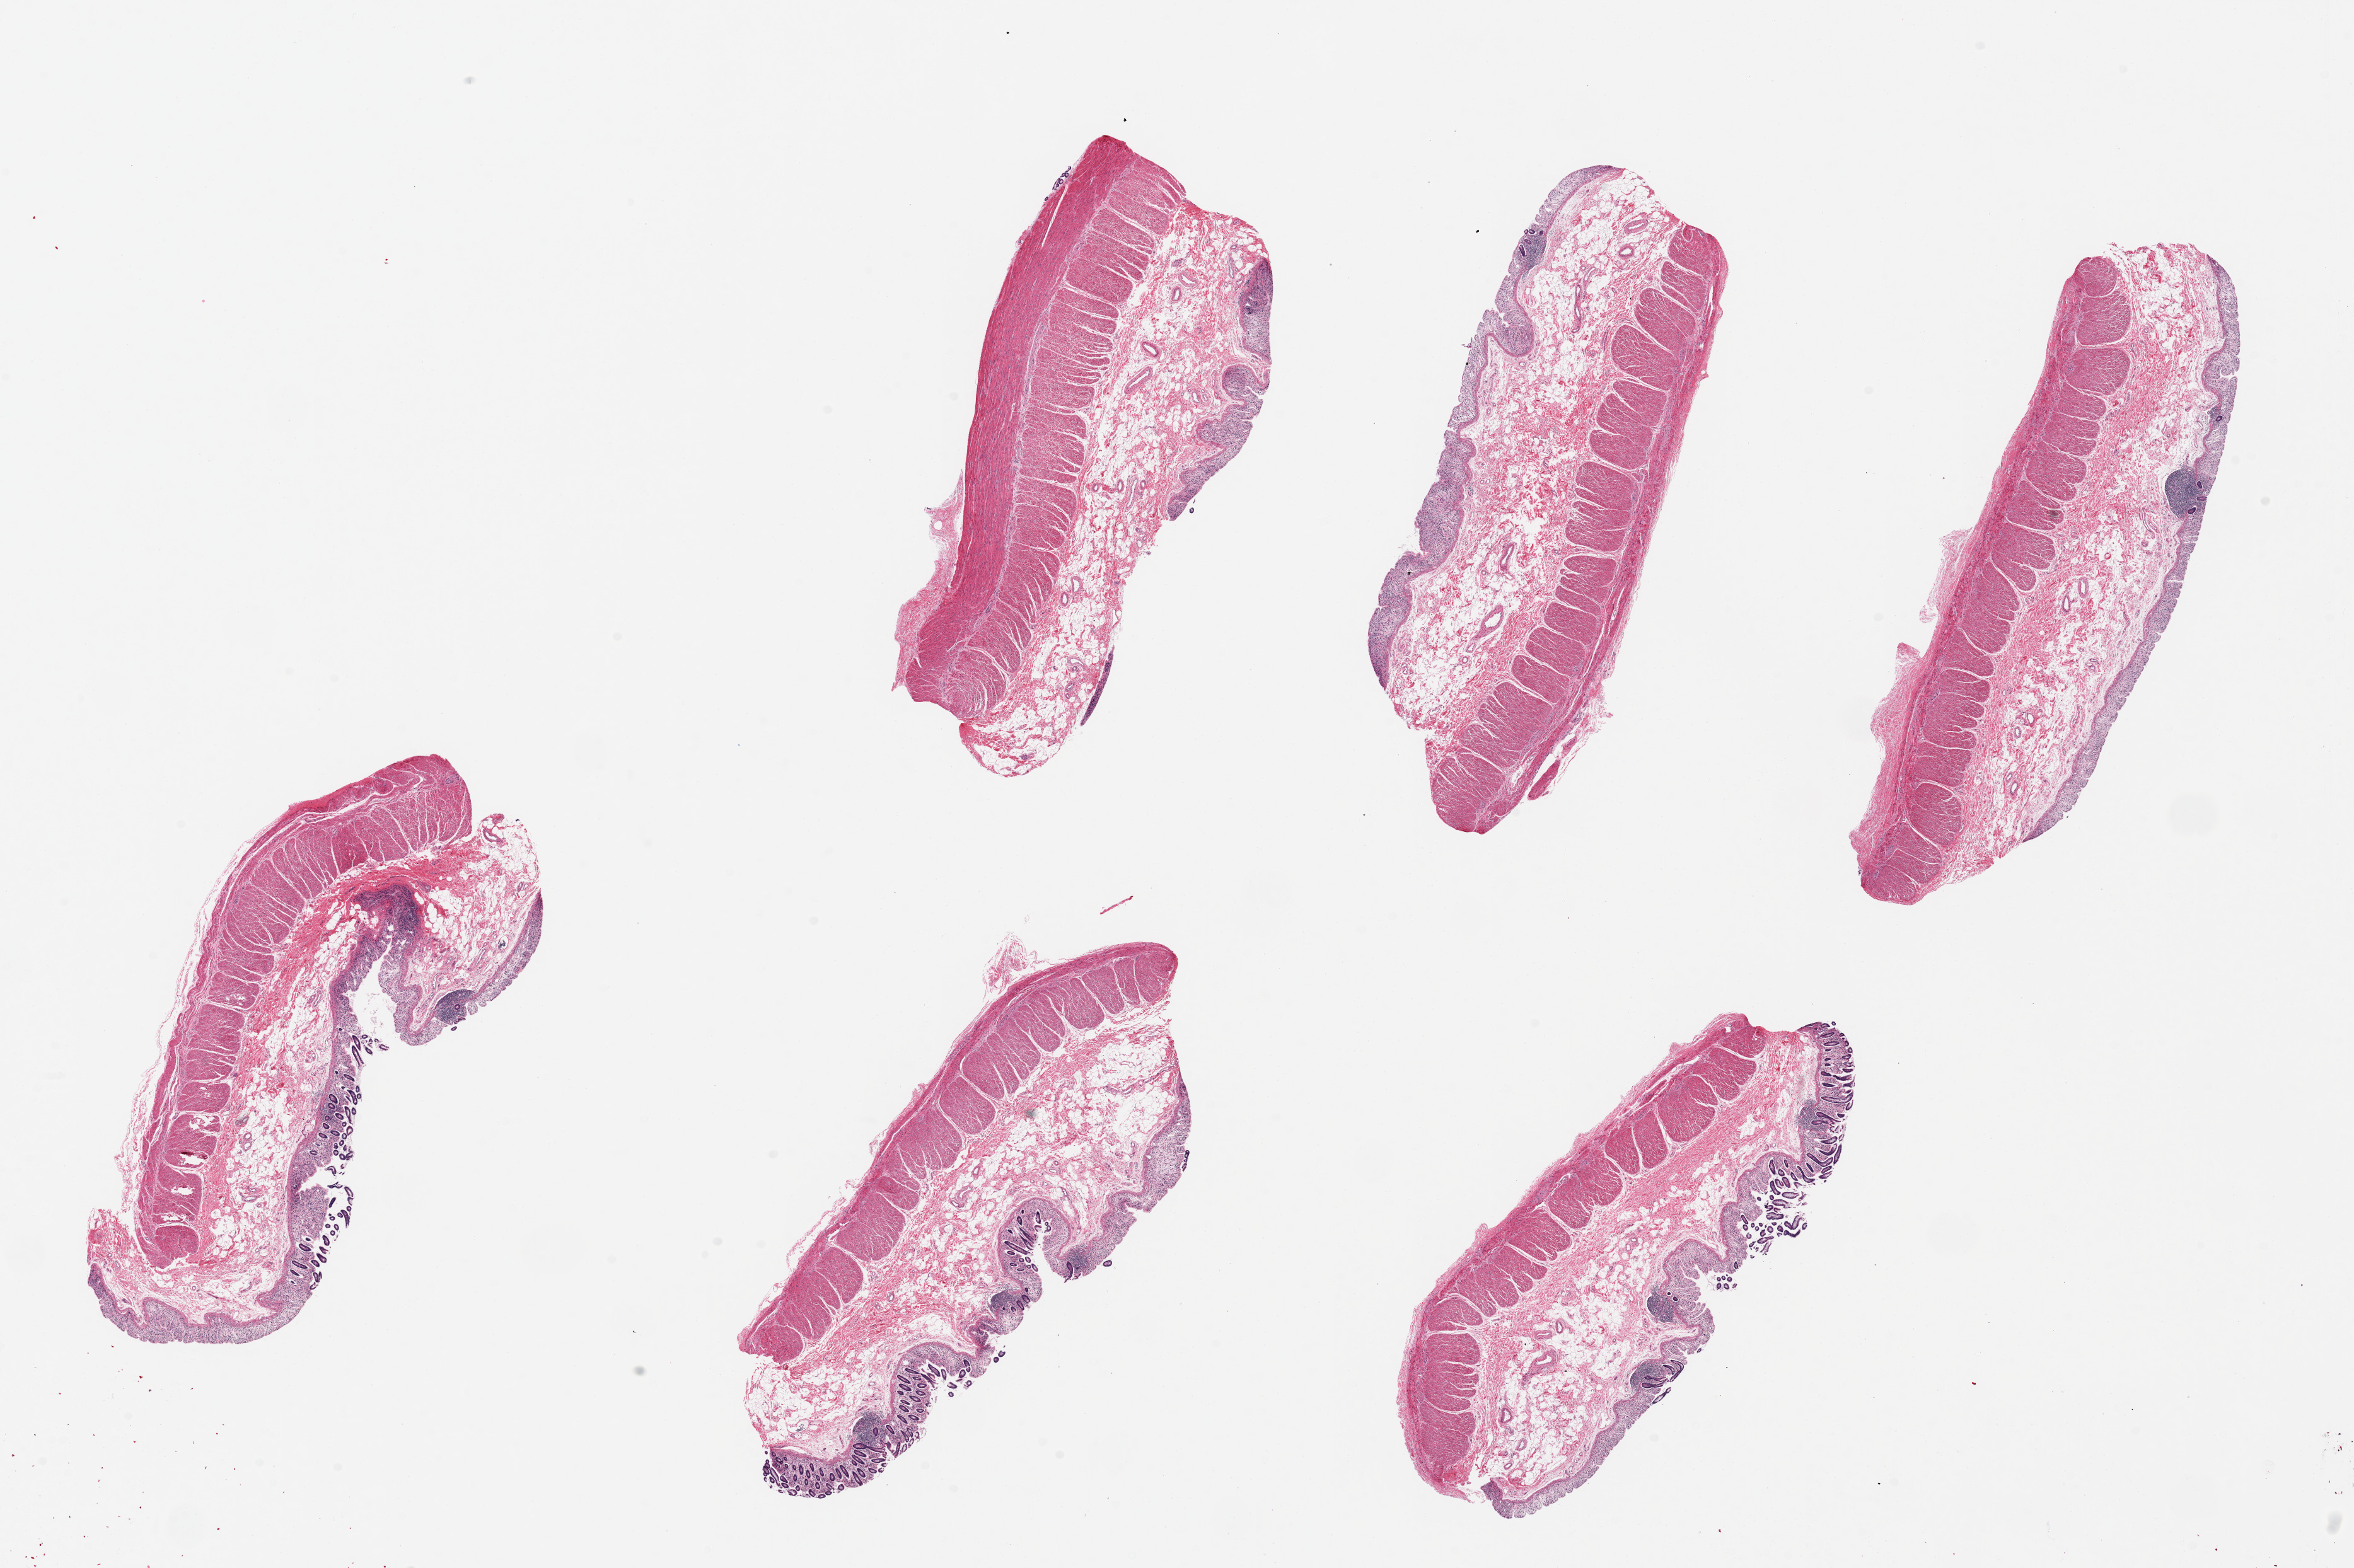
Digitized hematoxylin and eosin (H&E)-stained section, brightfield — low-resolution overview of the scanned area, about 29.5 x 19.7 mm; PAXgene-fixed, paraffin-embedded tissue; sampled site (target tissue): sigmoid colon; tissue donor sample. Donor: male.
Reviewer comment on this tissue sample: 6 pieces `8x3mm. Mucosa badly autolyzed ~5-10% thickness.